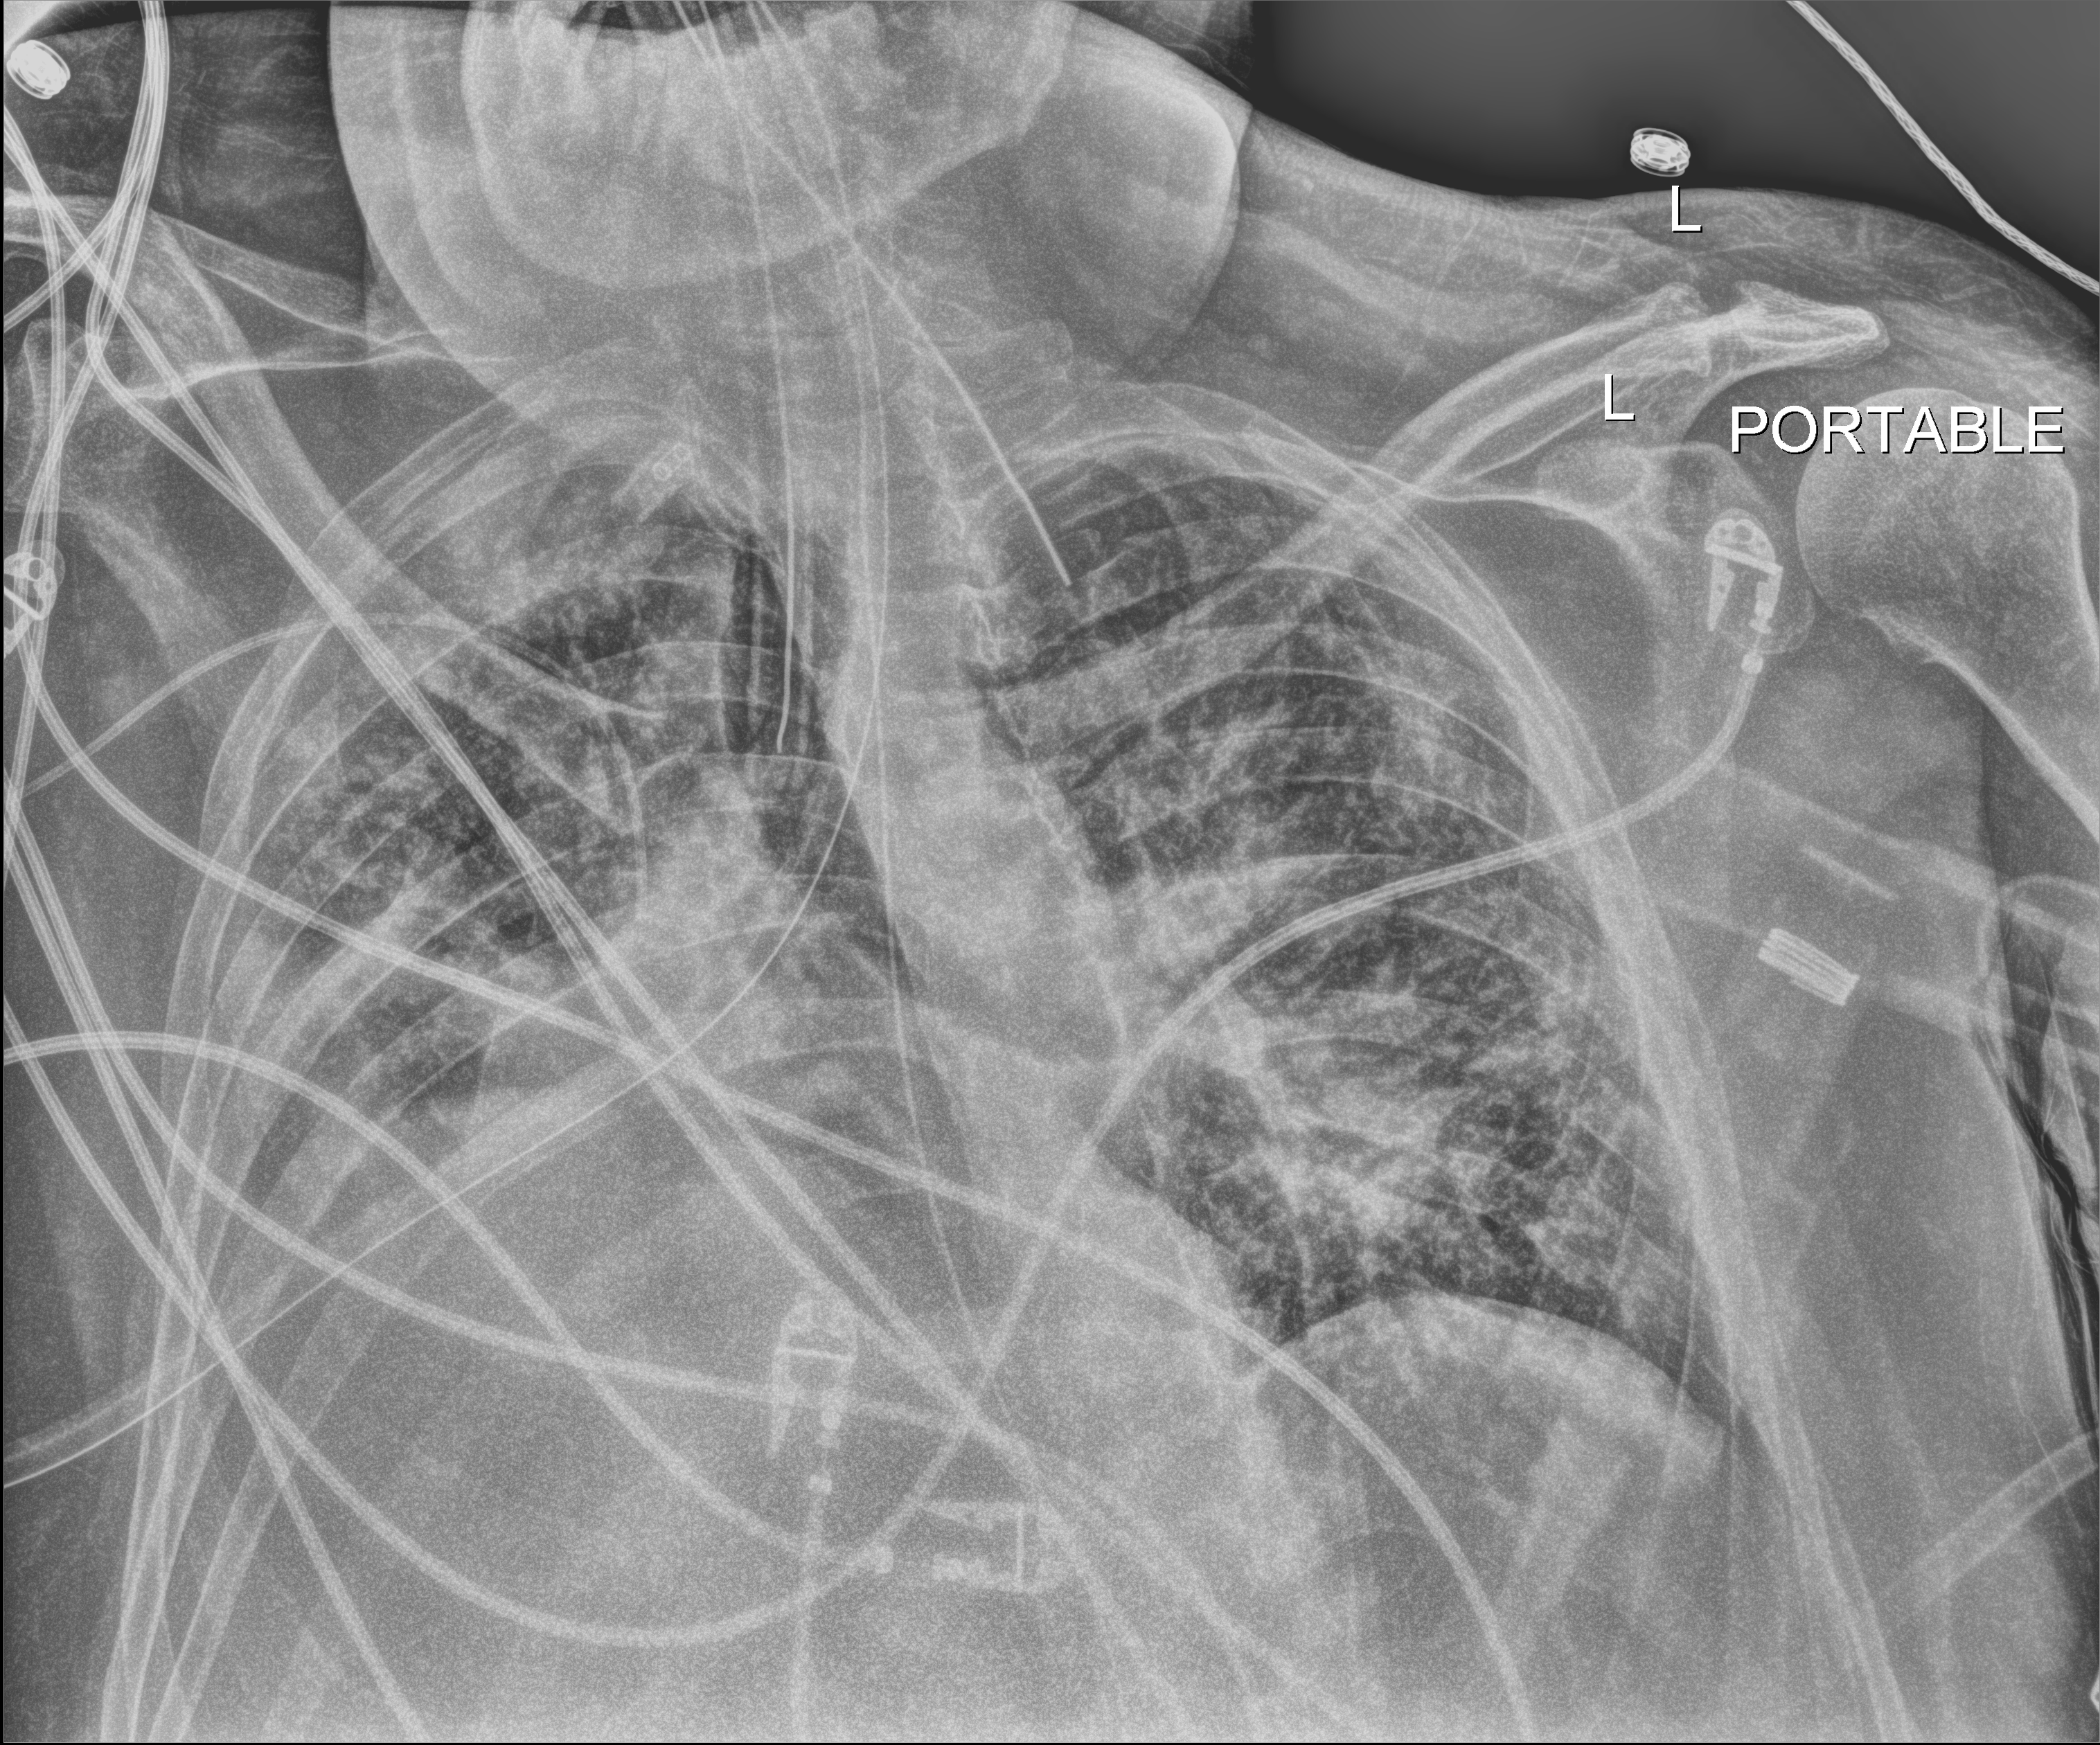
Portable chest radiograph; anteroposterior (AP) projection. Adult patient hospitalised with COVID-19, age 18–59 years.
Admission-level facts for this patient (not findings on this image; timing relative to this image not recorded): COPD (admission record): no; other chronic lung disease (admission record): yes.